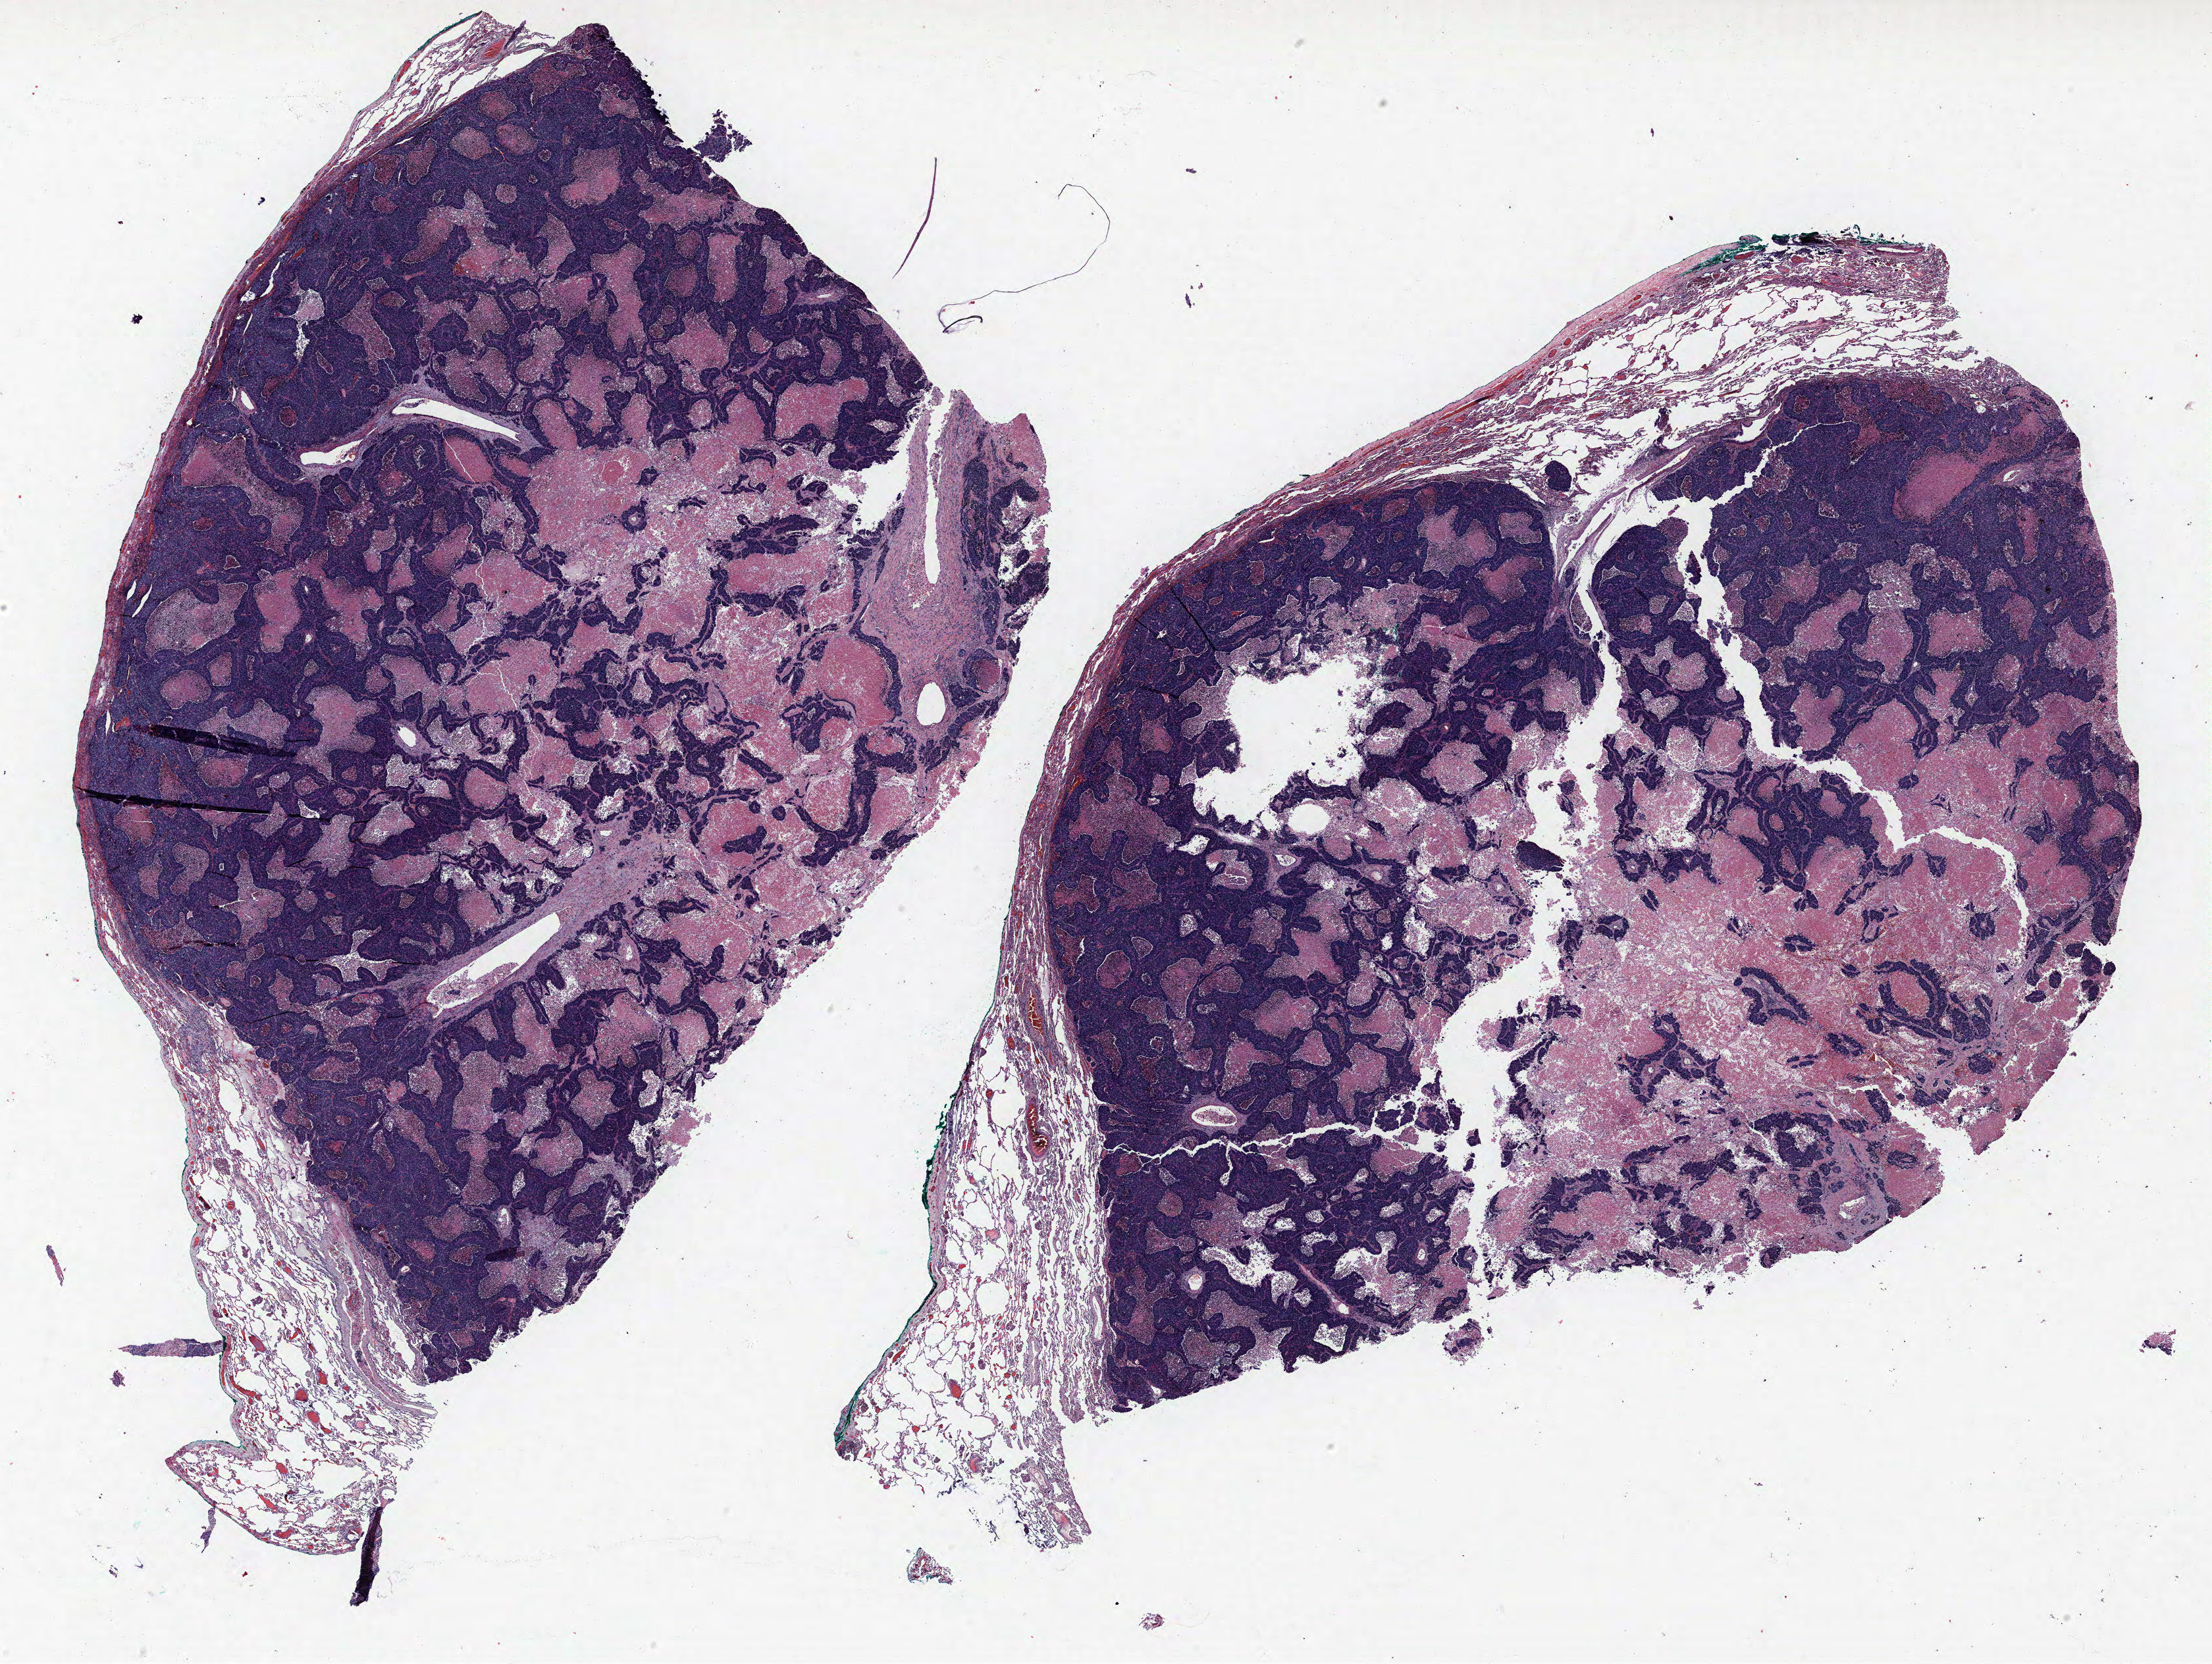
Whole-slide histology image, H&E-stained — whole scanned area (about 26.9 x 20.2 mm) shown as a low-resolution overview. Formalin-fixed paraffin-embedded (FFPE) section. Lung tissue. Male patient, aged 60 at enrolment. Current smoker at enrolment.
Participant's lung-cancer diagnosis: Large cell neuroendocrine carcinoma.